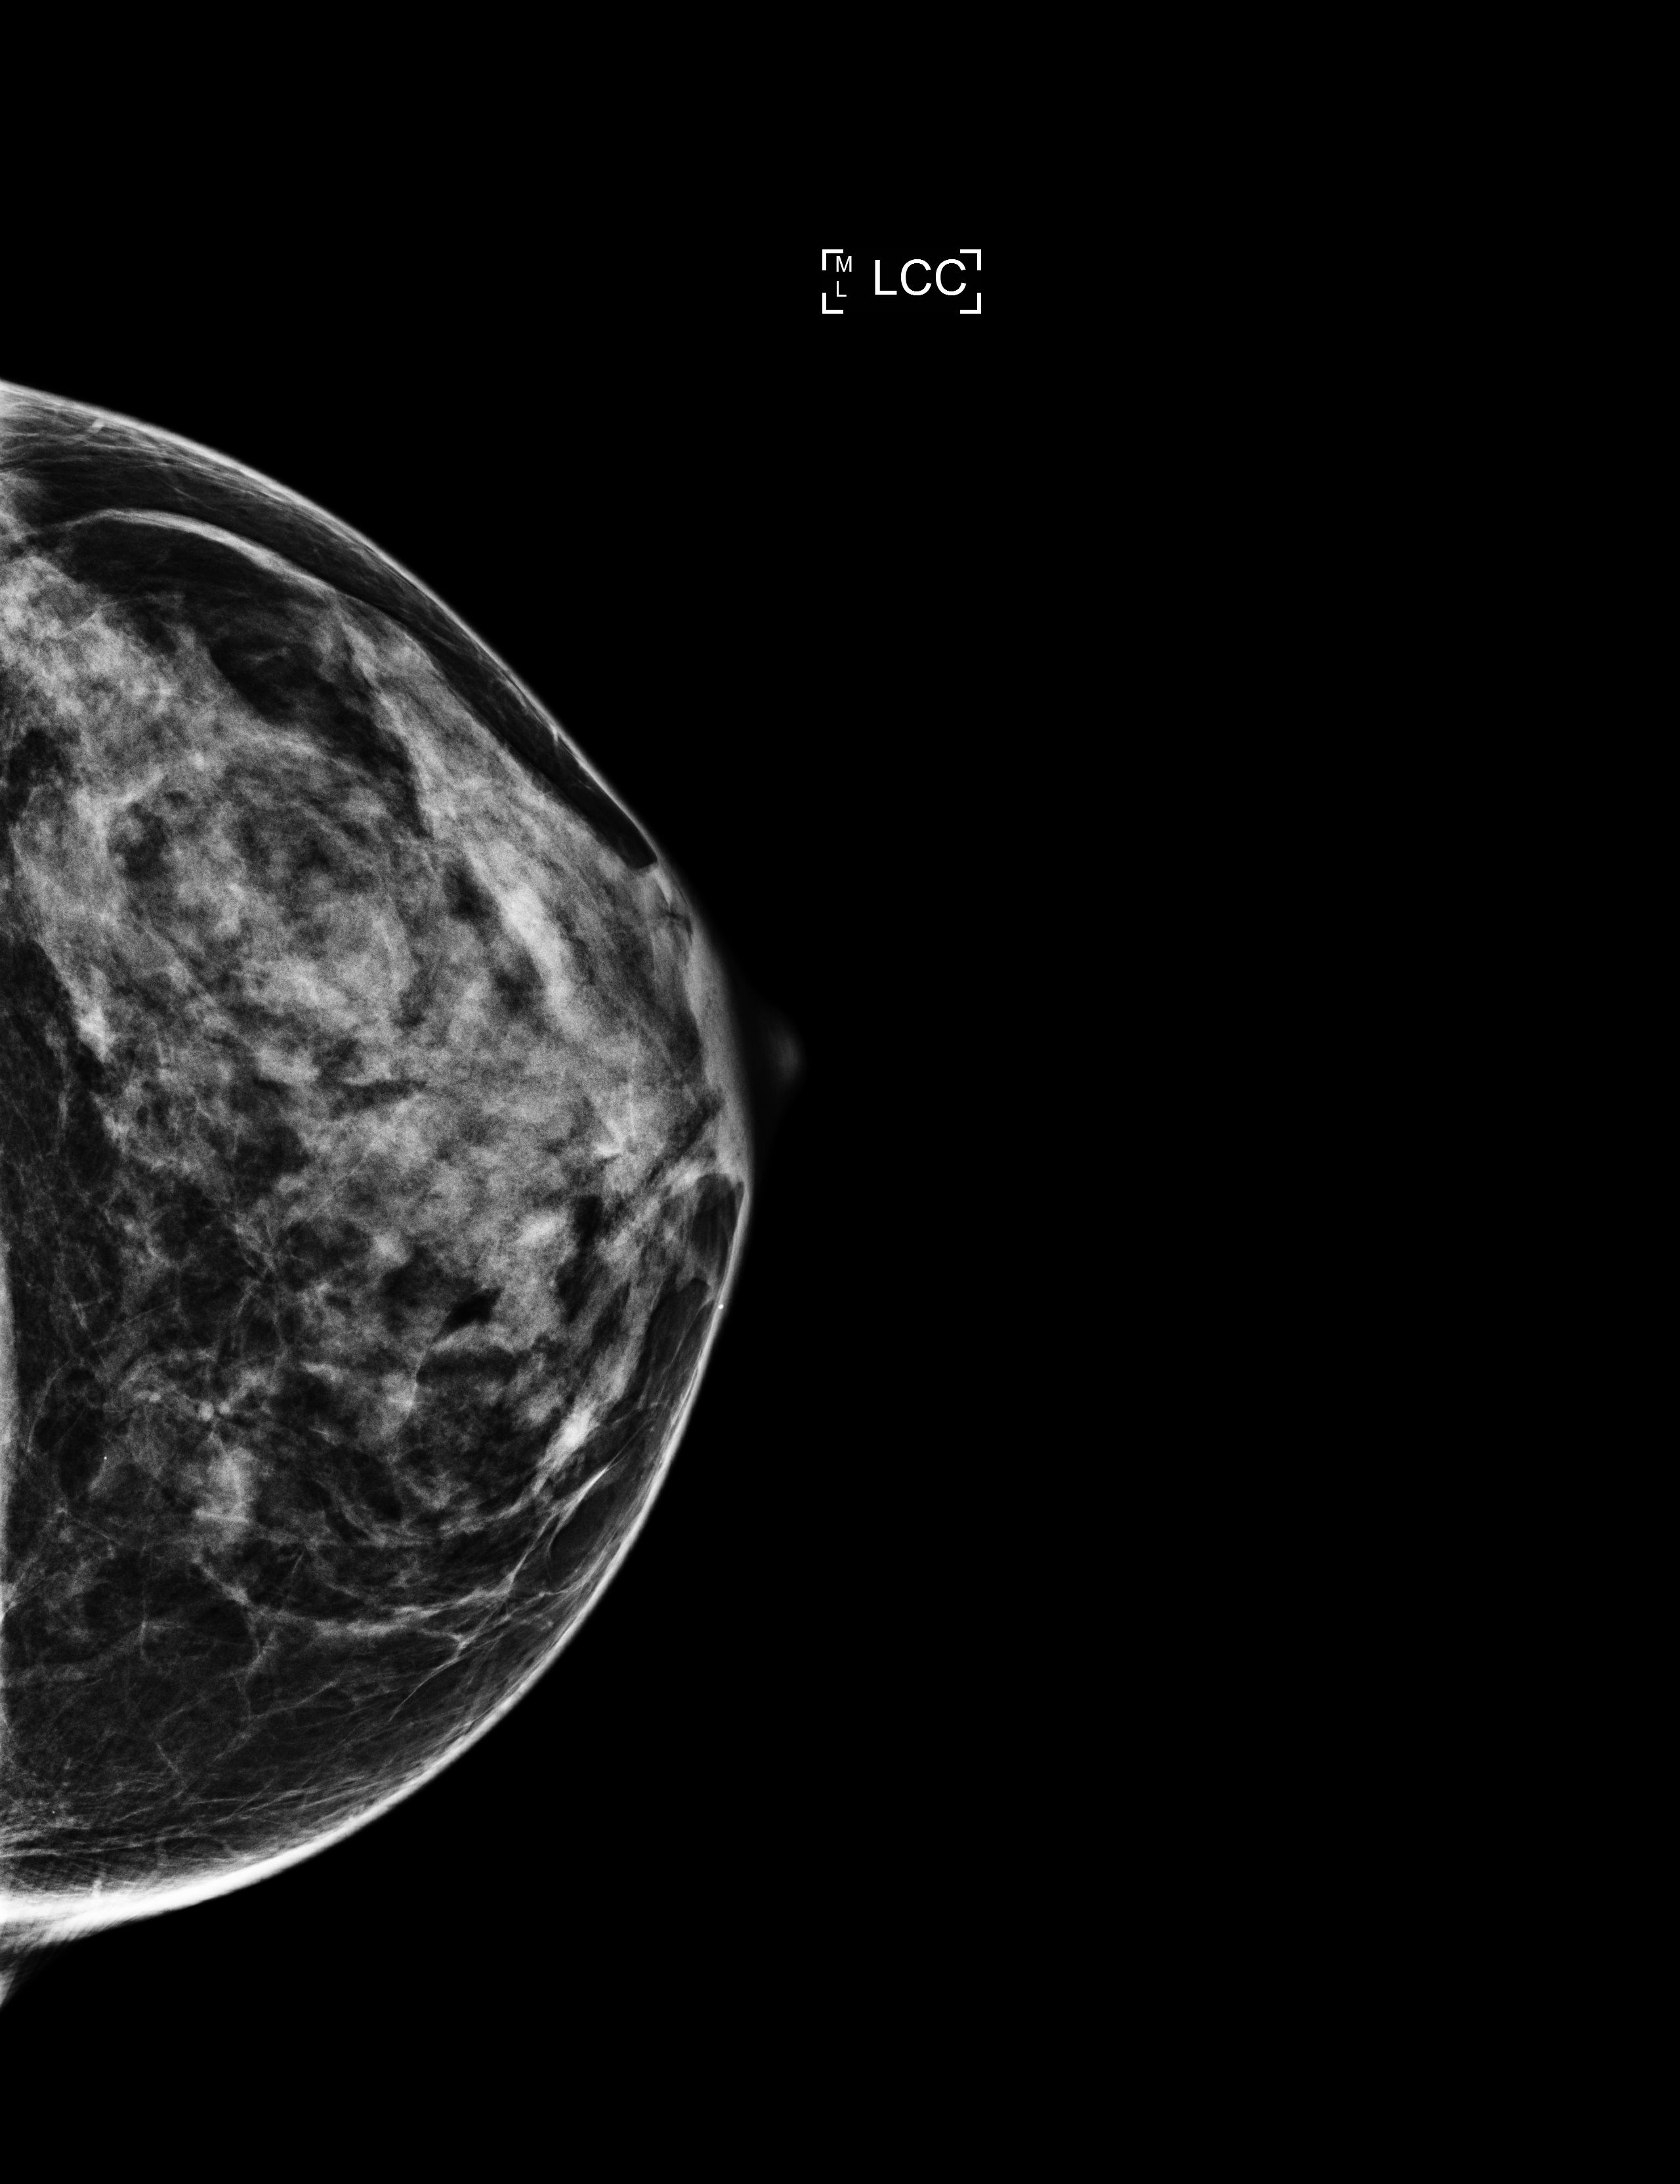
Annual screening mammography examination; system: Selenia Dimensions. Patient: female, 53 years.
Image type: full-field digital mammogram. Breast: left. Projection: craniocaudal (CC) view.